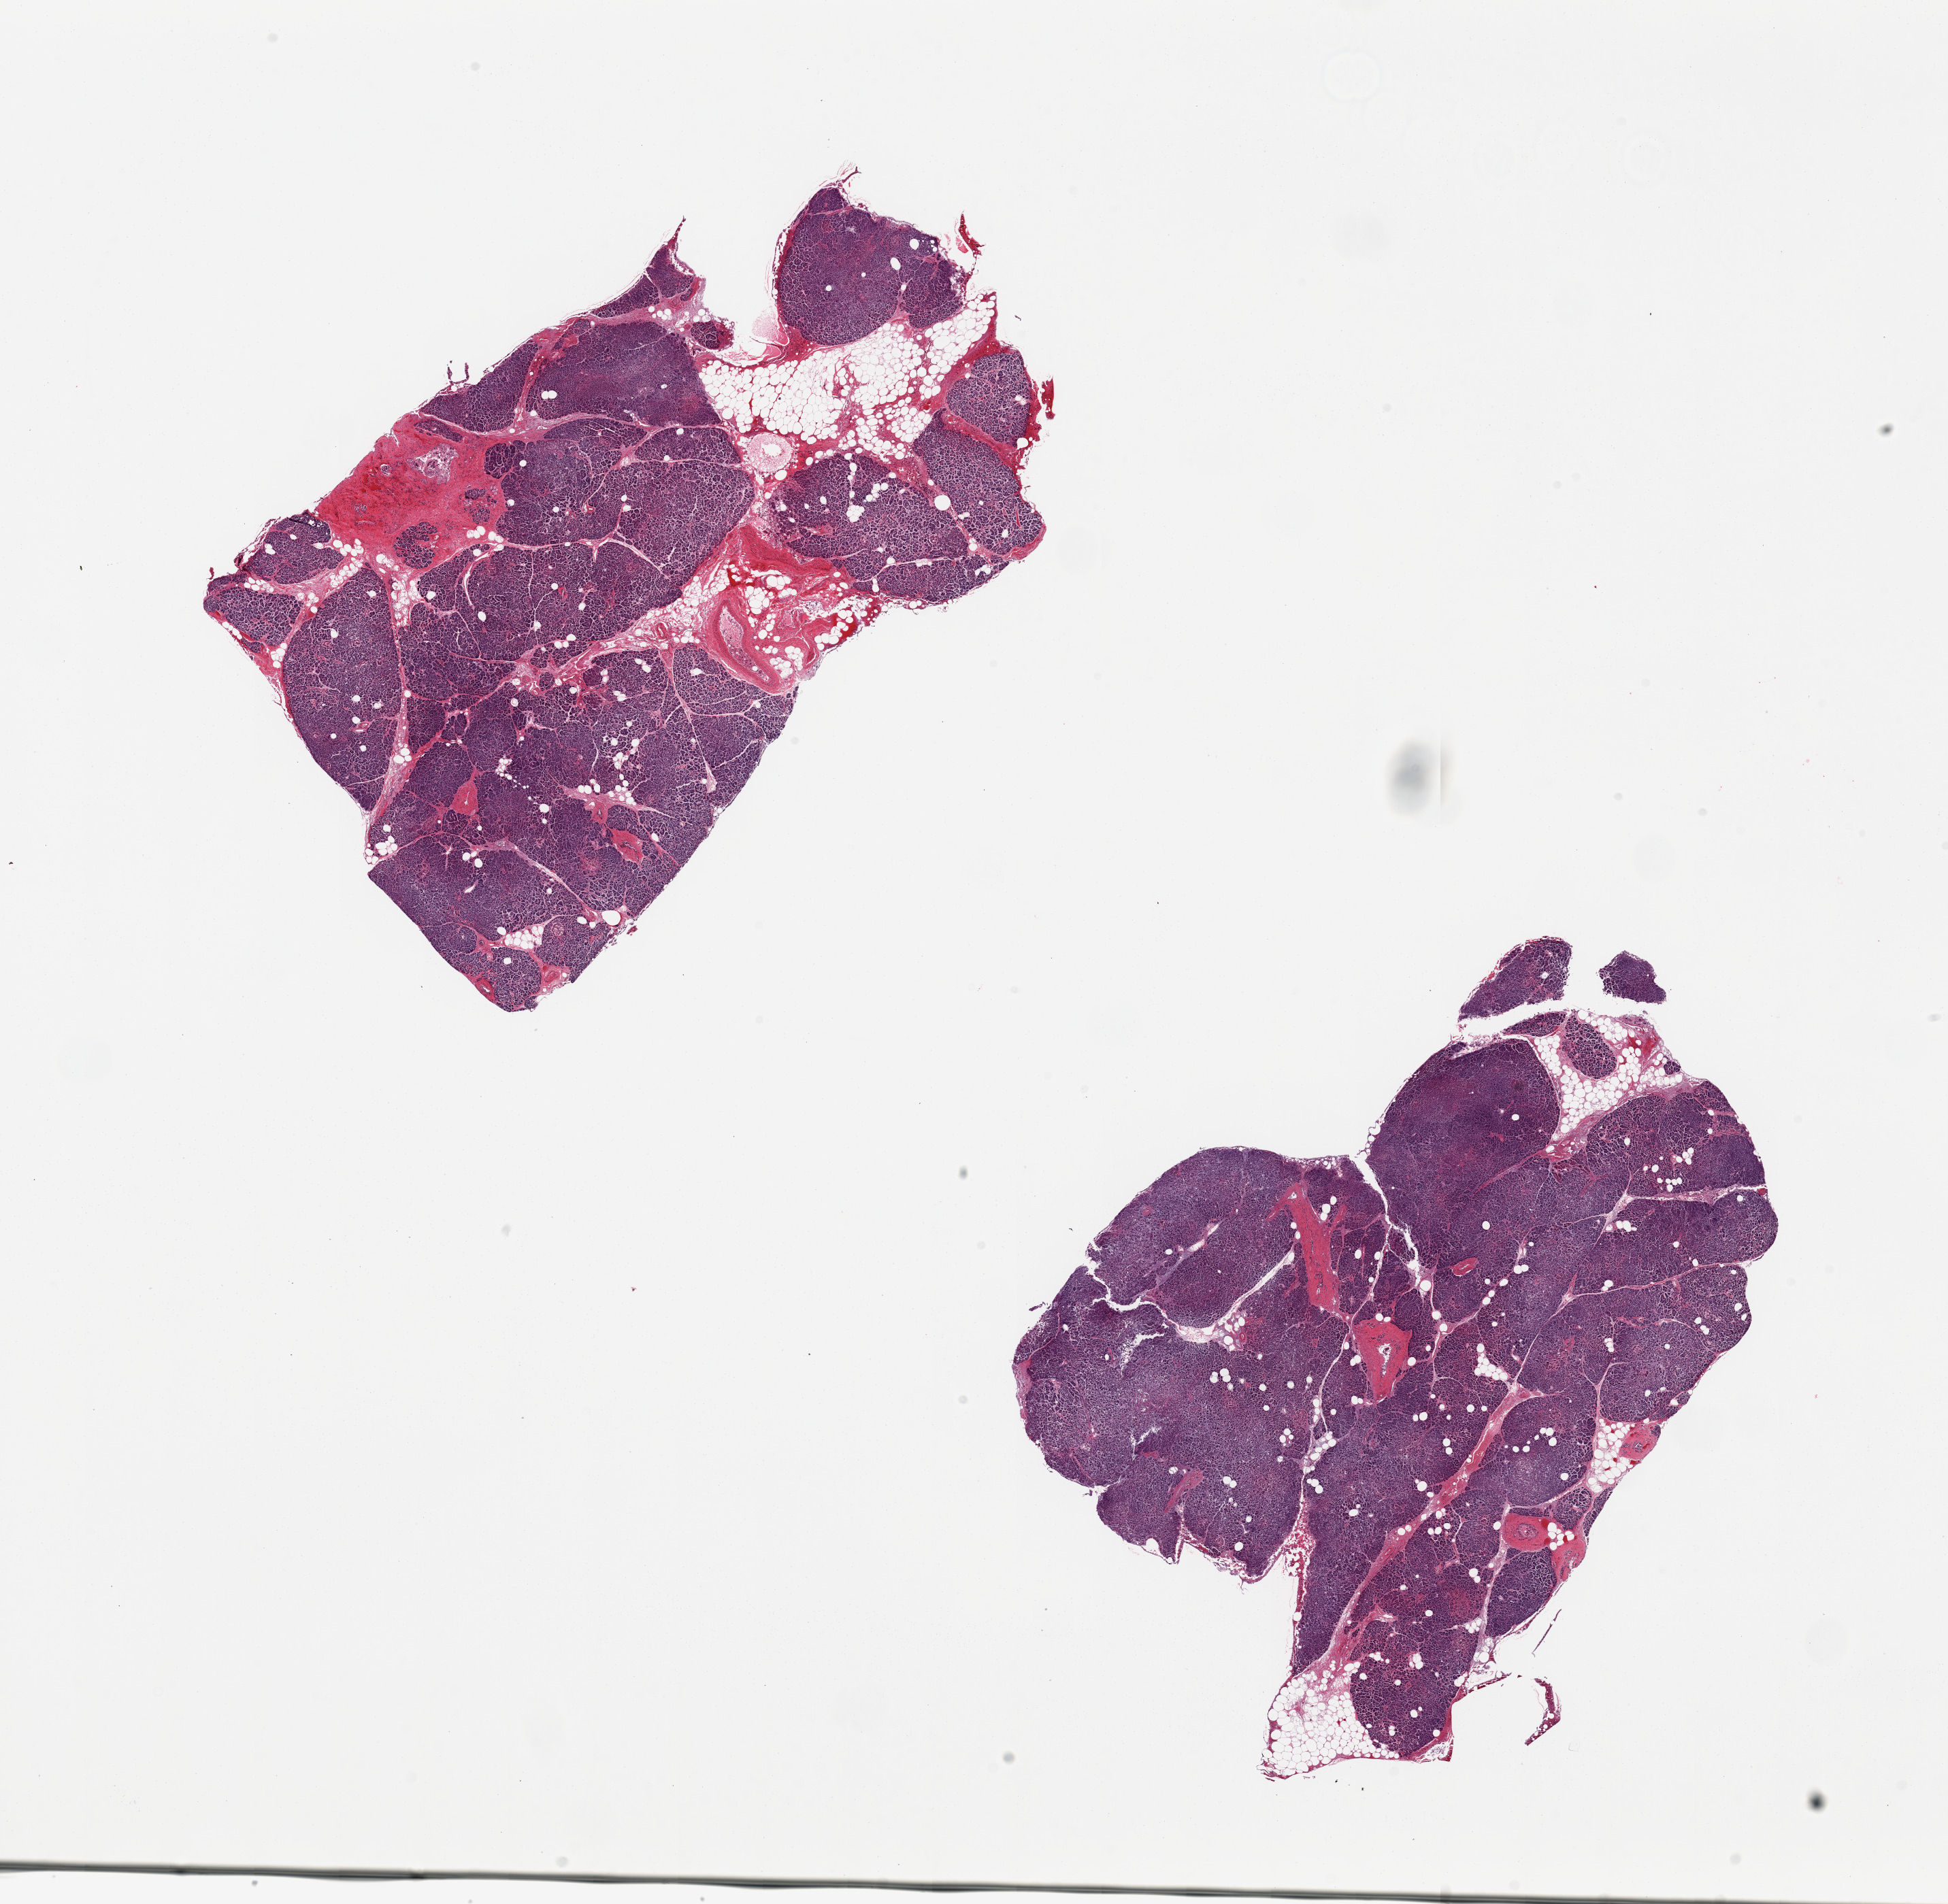
Whole-slide image, hematoxylin and eosin (H&E) stain — whole scanned area (about 22.6 x 22.1 mm) shown as a low-resolution overview, PAXgene-fixed paraffin-embedded (PFPE) section, section of pancreas (target tissue), donor tissue sample. Donor: male.
Pathologist's review note for this sample: 2 pieces; 10% internal fat; islets appear reduced in number.